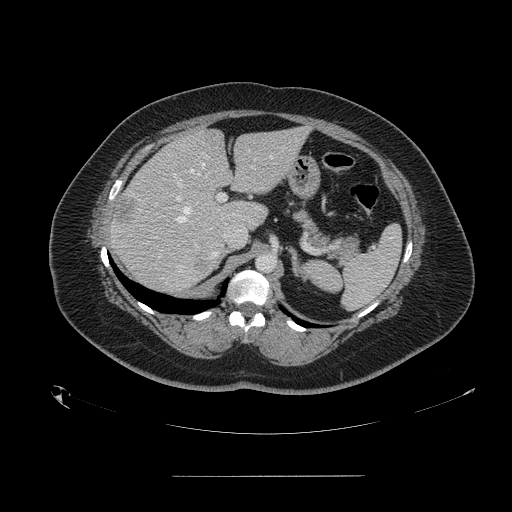
Contrast-enhanced abdominal CT, one axial slice; position 99 of 164 along the scan axis; intravenous contrast given; soft-tissue window (W 400 / L 40 HU); 2.5 mm slice thickness; 512 × 512 image matrix. Female patient, age 52 years. Case-level facts recorded for this patient, not image findings: diagnosis: colorectal cancer liver metastases, imaged before liver resection; multiple liver metastases: yes.
Structures marked on this image (manually delineated by an expert):
- hepatic veins: bounding box <177,156,272,222> (left, top, right, bottom; pixels)
- liver: <111,129,307,293>
- planned liver remnant (the part of the liver to remain after resection): <175,128,307,229>
- portal vein (with intrahepatic branches): <171,174,226,202>
- liver metastasis: <196,260,208,272>
- liver metastasis: <115,197,135,226>